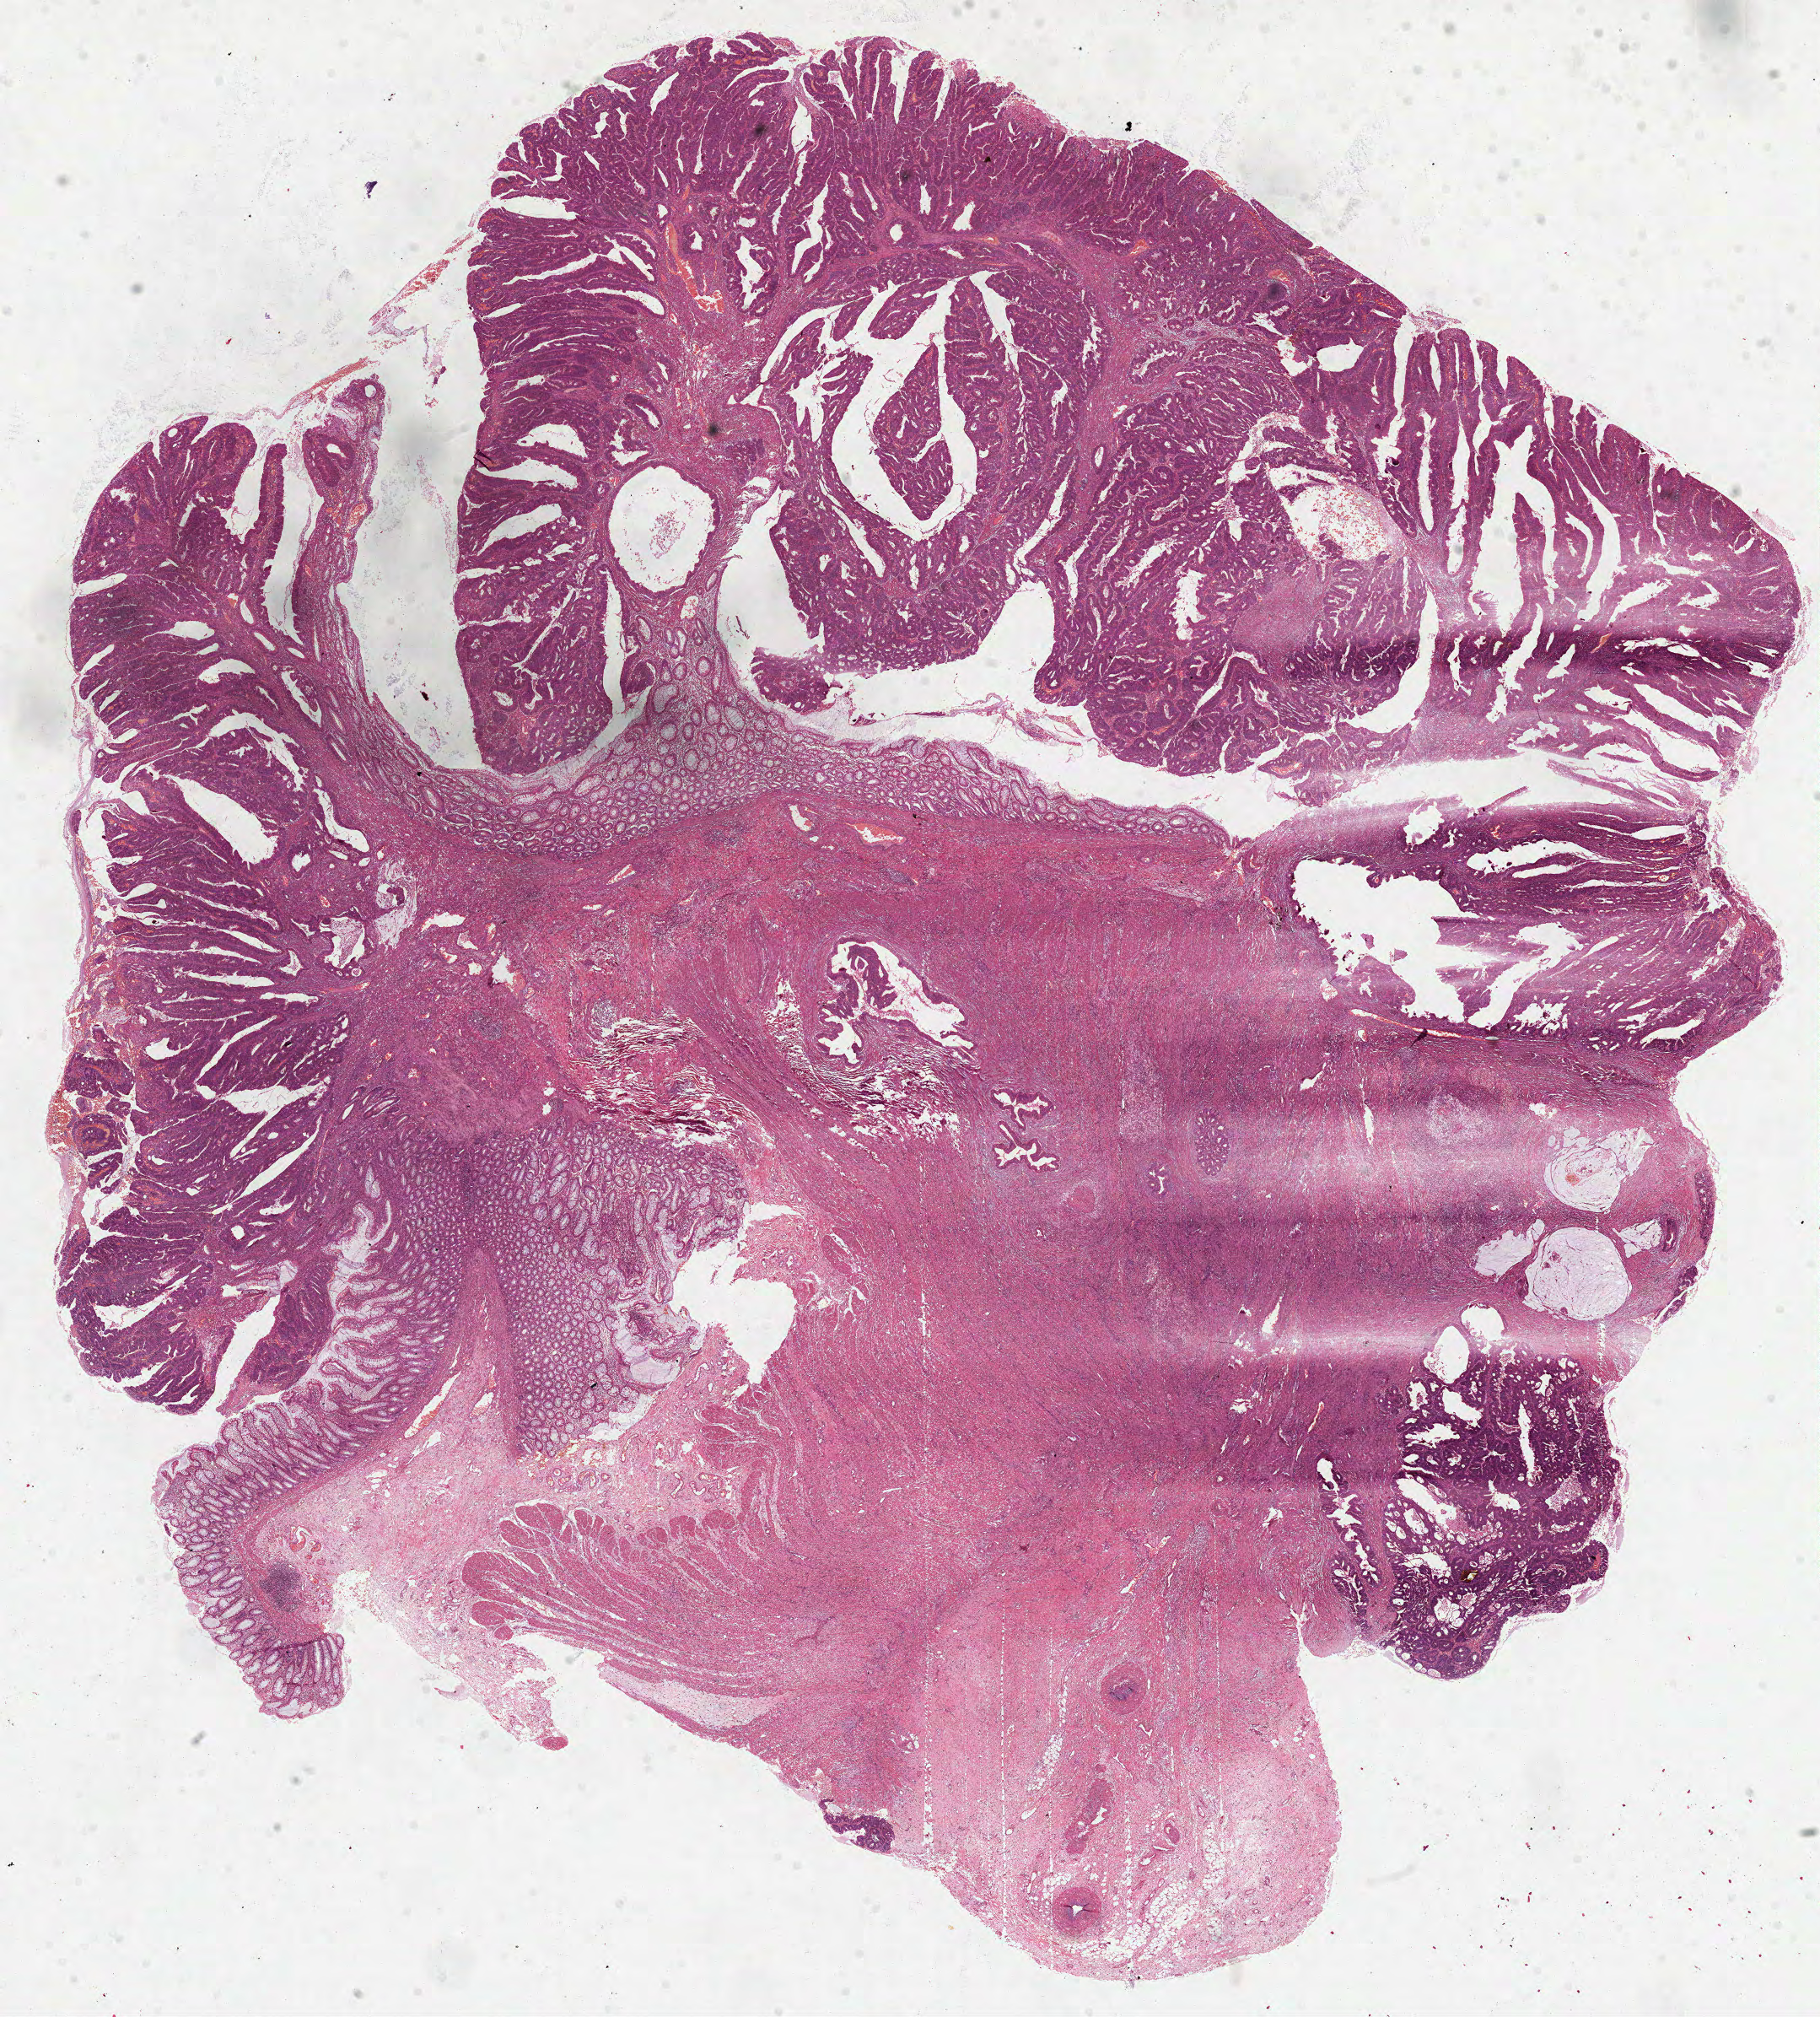
Digitized Hematoxylin and eosin (H&E) stained tissue section (whole slide) — low-resolution overview of the scanned area, about 17.4 x 19.3 mm, FFPE section, colon, primary tumour sample. Patient: male, age at initial diagnosis 65 years.
AJCC pathologic stage: IIA (6th edition). TNM: T3 N0 M0. Histologic diagnosis: Papillary adenocarcinoma, NOS (ascending colon).